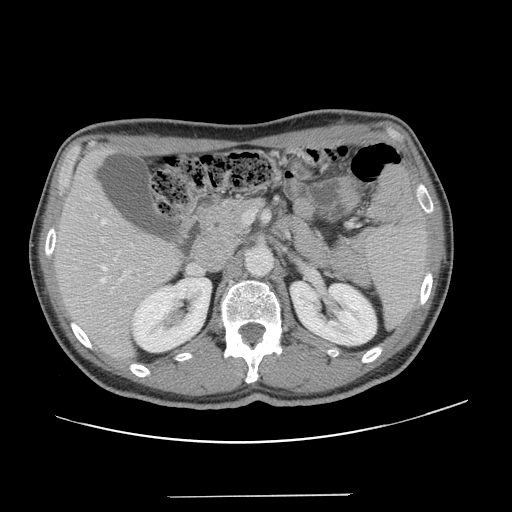
Contrast-enhanced abdominal CT, one axial slice. Position 74 of 131 along the scan axis. 120 kVp. Intravenous contrast given. Soft-tissue window (W 400 / L 40 HU). 2.5 mm slice thickness. 512 × 512 image matrix. Male patient, age 60 years. From the clinical record (not read from this slice): diagnosis: colorectal cancer liver metastases, imaged before liver resection; multiple liver metastases: no; largest metastasis: 2.5 cm; disease in both lobes: no.
Outlined on this slice (expert manual segmentation):
- hepatic veins: bounding box [x1, y1, x2, y2] px = [101, 219, 117, 283]
- liver: [55, 151, 180, 360]
- planned liver remnant (the part of the liver to remain after resection): [55, 151, 180, 359]